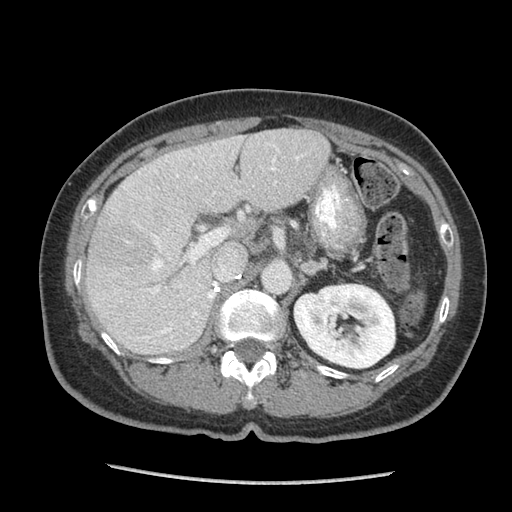
Contrast-enhanced abdominal CT (liver protocol), one axial slice. Position 47 of 105 along the scan axis. Soft-tissue window (W 400 / L 40 HU). 512 × 512 image matrix, field of view 340 × 340 mm. From the clinical record (not read from this slice): diagnosis: hepatocellular carcinoma (patient treated with transarterial chemoembolisation; whether this scan precedes or follows treatment is not stated here); TNM stage (as recorded): Stage-I; Child-Pugh class: A; tumour size: 11.1 cm.
Structures marked on this image (semi-automatically segmented with operator editing):
- liver parenchyma outside the tumour (the mass and vessels are separate outlines, so this box may not span the whole liver): bounding box [x1, y1, x2, y2] px = [86, 128, 330, 354]
- mass: [90, 216, 153, 278]
- liver vessels: [124, 145, 299, 339]